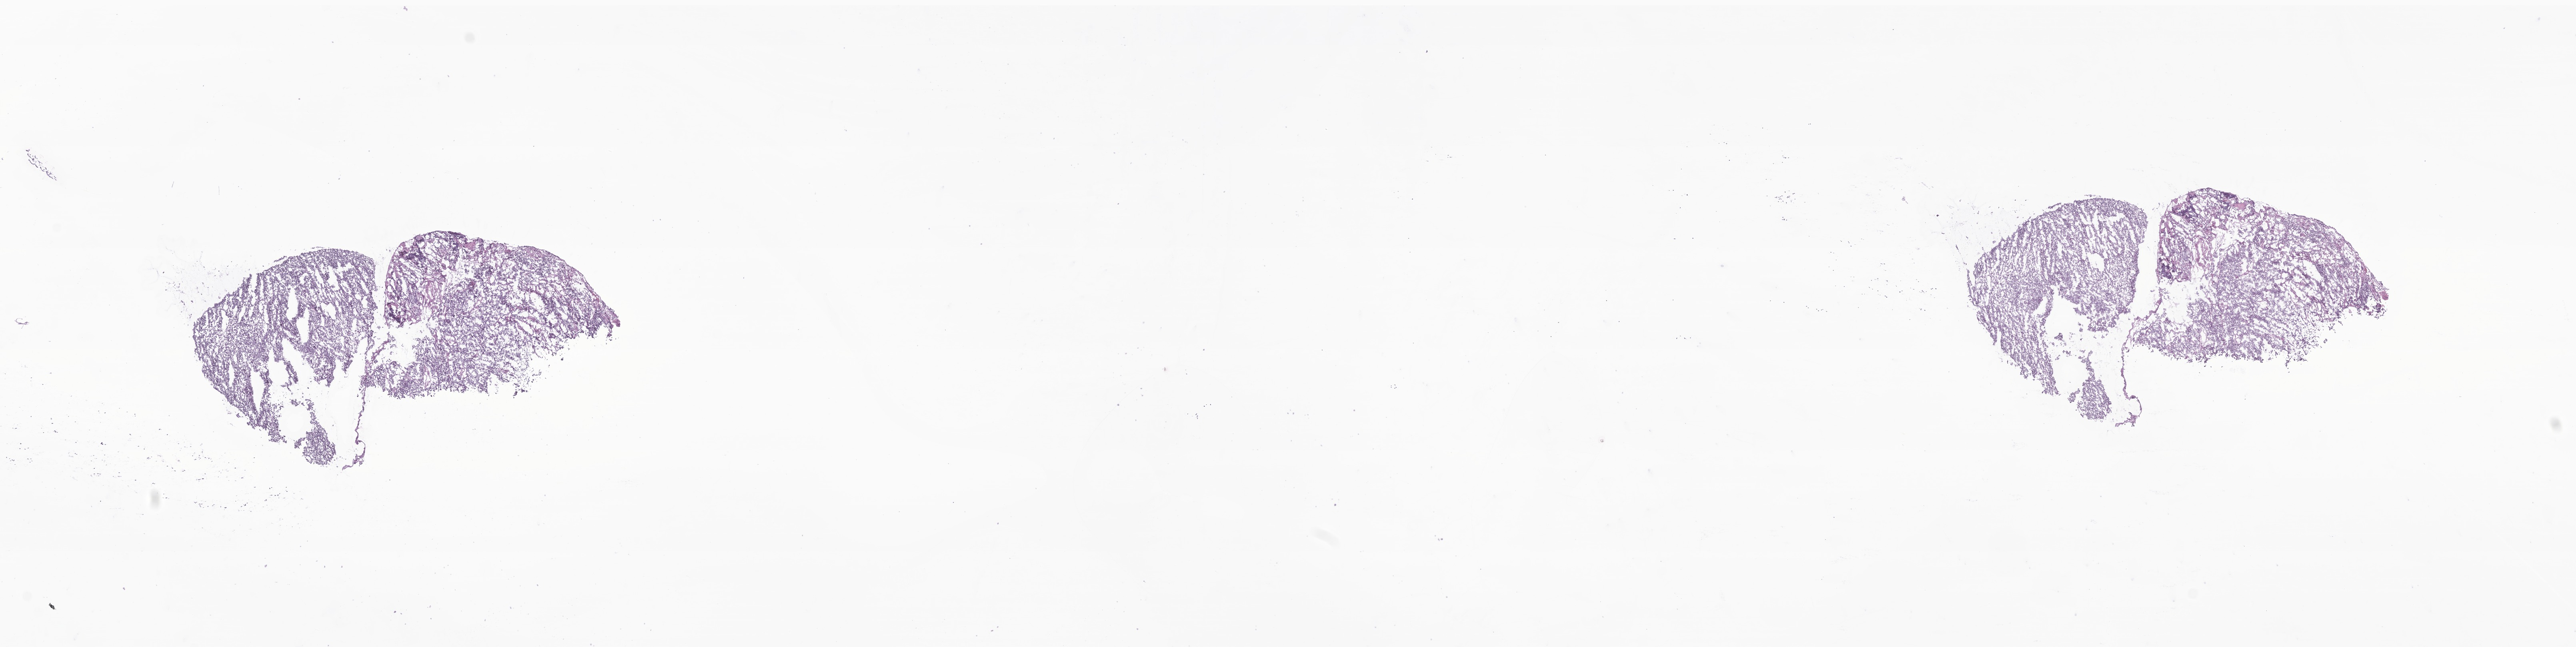
Digitized haematoxylin and eosin-stained section of tumor tissue from the pineal gland, low-resolution overview of the scanned area, about 27.1 x 6.8 mm; frozen section (OCT-embedded). Patient male; age 39 months.
Diagnosis: Pineoblastoma.